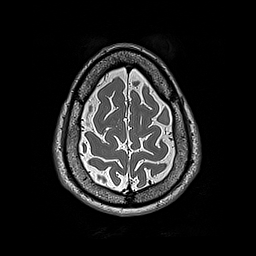
Brain MRI from a brain-tumour surgery series, one axial slice. Slice 52 of 192 in the series (ordered by position). 1 mm slice thickness. 256 × 256 image matrix. Case-level facts recorded for this patient, not image findings: histopathology: Astrocytoma; WHO grade: 2; IDH mutation: yes.
Structures marked on this image (manually delineated by an expert):
- tumour: bounding box (x1, y1, x2, y2) in pixels: (159, 110, 167, 122)